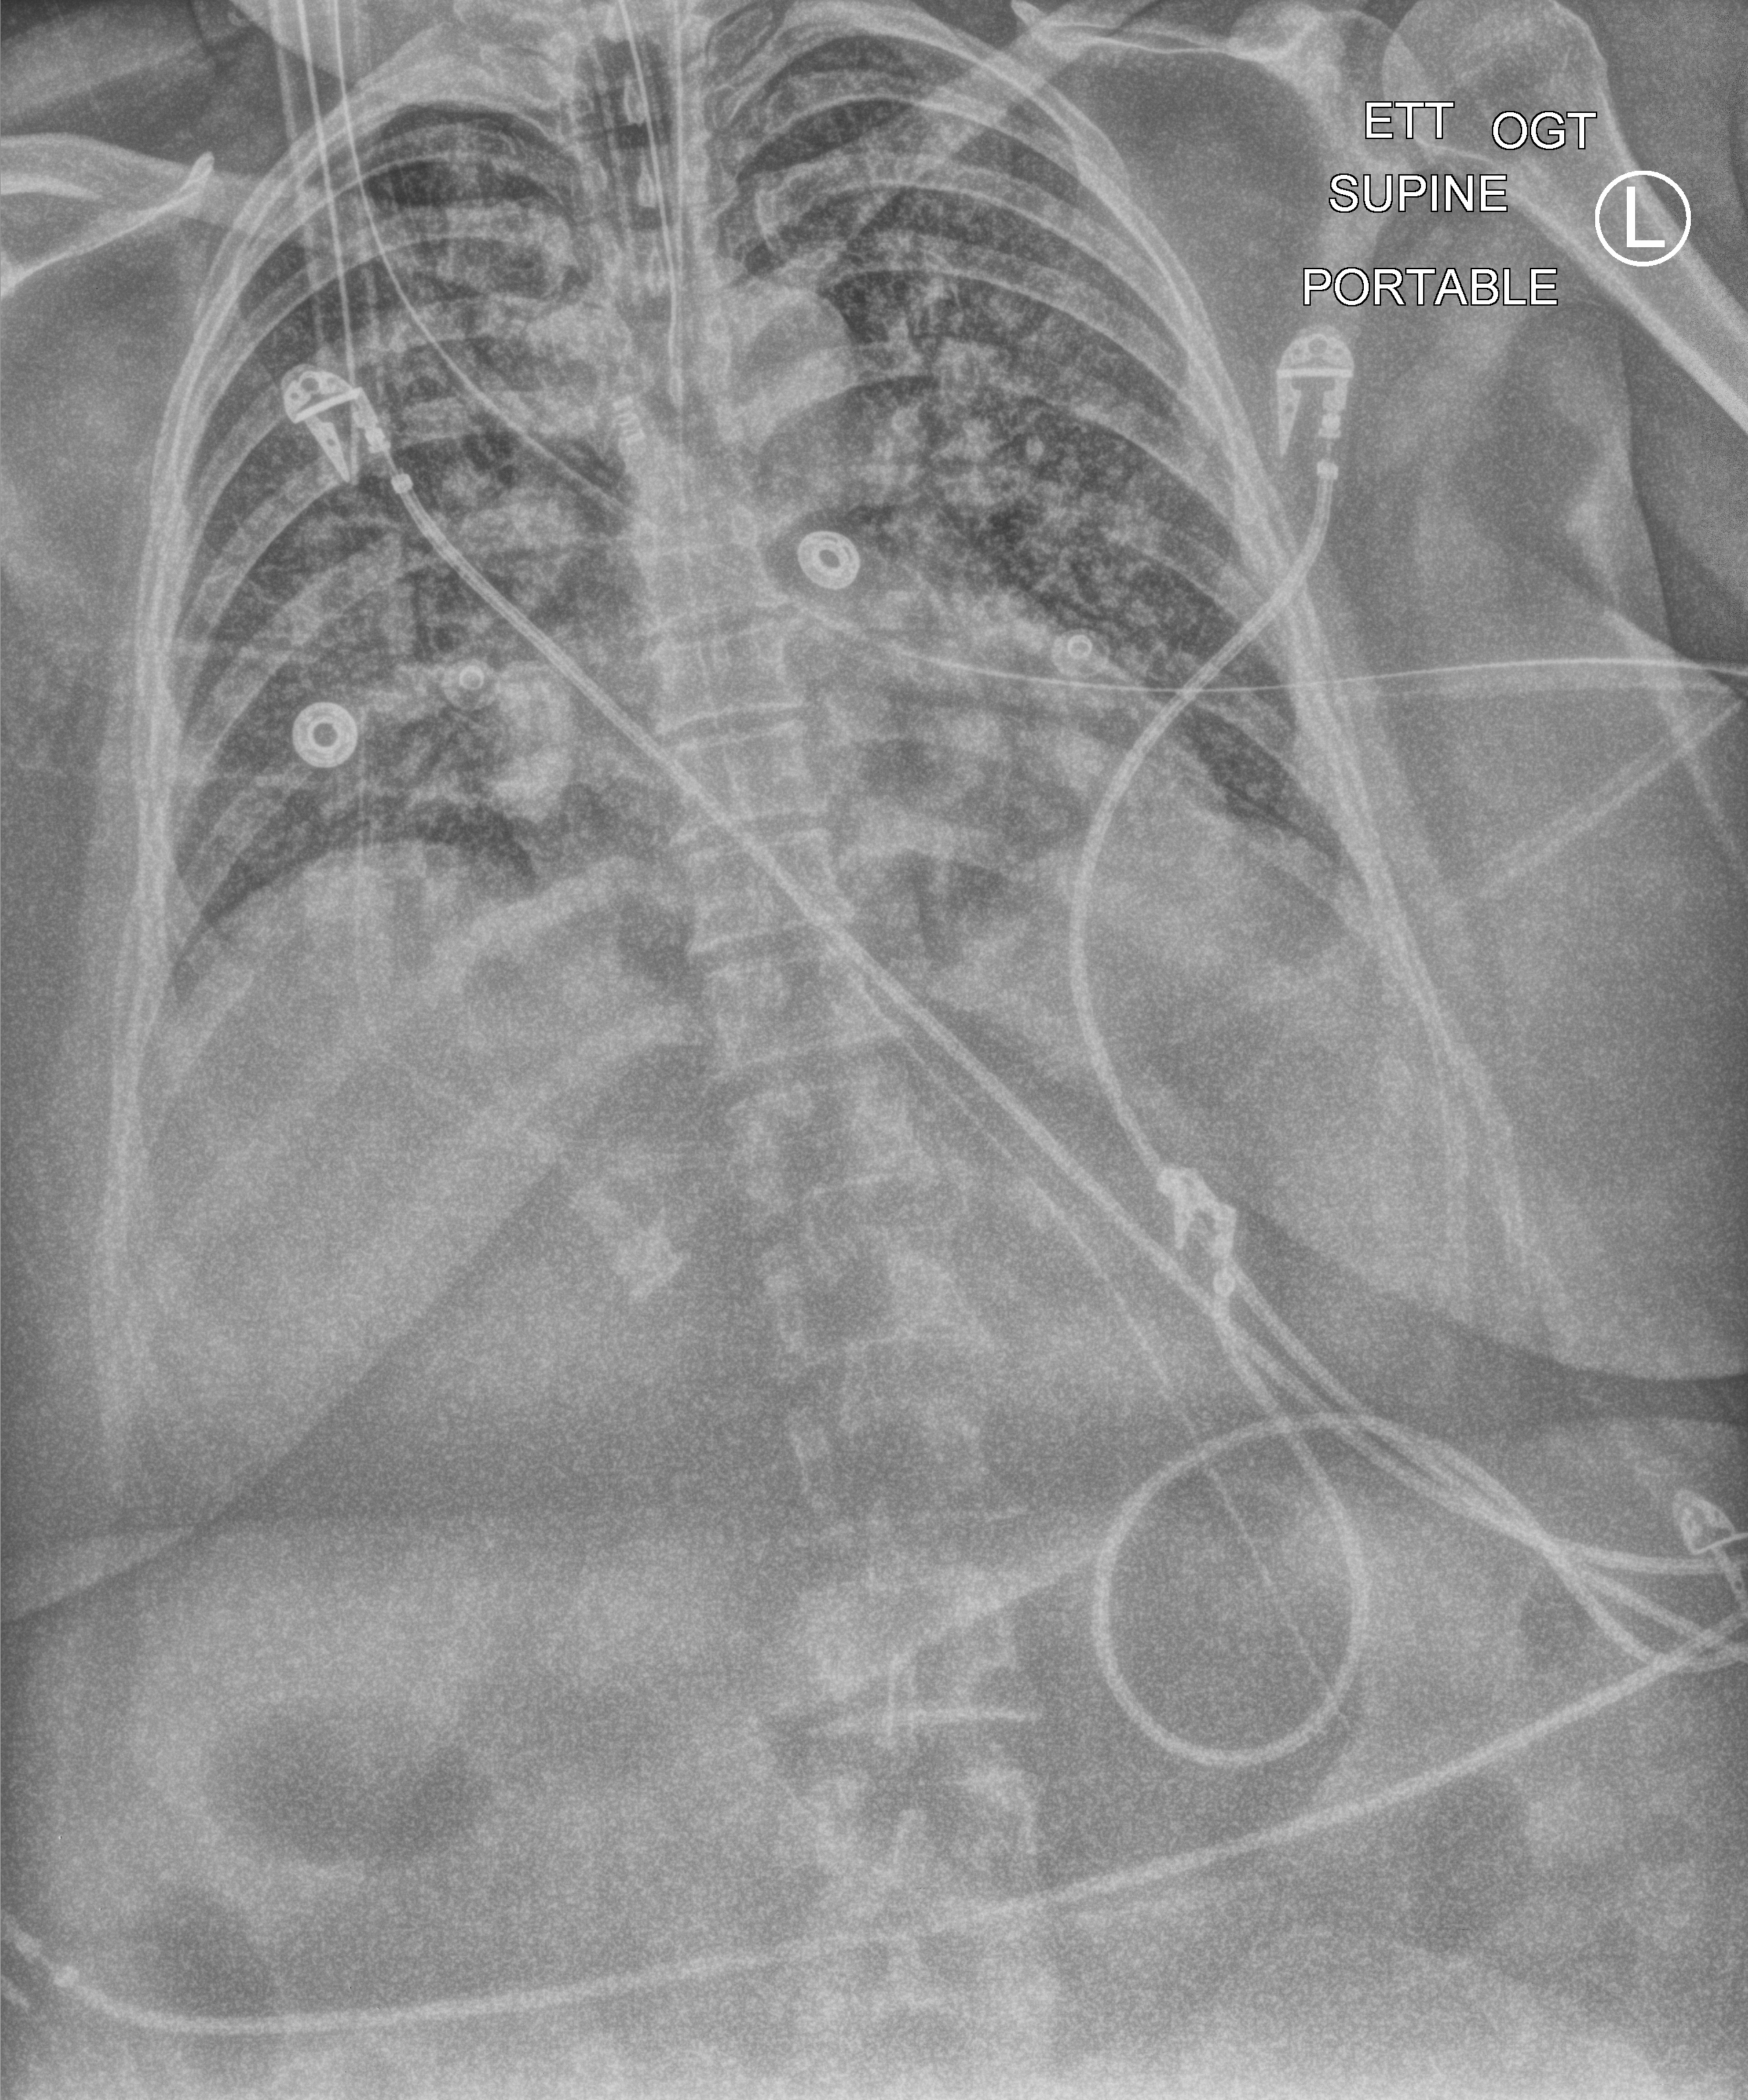
Chest X-ray (portable). Female patient hospitalised with COVID-19, age 18–59 years.
Hospital-stay facts (about this admission, not read from this image; timing relative to this image not recorded):
- hypertension (admission record): yes
- smoking status (admission record): never